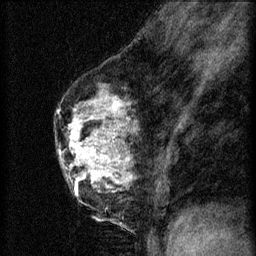
Breast MRI (dynamic contrast-enhanced), one sagittal slice. Slice 38 of 60 in the series (ordered by position). 3 images stored at this slice position (order not interpretable as contrast timing). 1.5 T. TE 4.2 ms, TR 8.2 ms. 2 mm slice thickness. 256 × 256 image matrix, field of view 180 × 180 mm. Female patient, age 56 years.
Annotated regions visible in this slice (semi-automatic segmentation, software-assisted and operator-edited):
- analysis volume of interest (the breast-tissue region the enhancement analysis was run in; not a lesion): bounding box (x1, y1, x2, y2) in pixels: (60, 124, 114, 179)
- tumour enhancement mask (voxels above the 70 % enhancement threshold inside the analysis volume of interest): (77, 124, 96, 179)